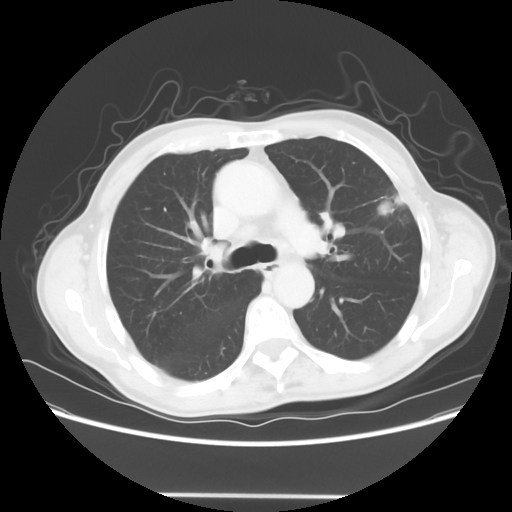
Chest CT, one axial slice; position 41 of 64 along the scan axis; 120 kVp; lung window (W 1500 / L -600 HU); 5 mm slice thickness; 512 × 512 image matrix. Patient: male, 71 years. From the clinical record (not read from this slice): clinical TNM (as recorded): T1c N0 M0; histopathological grade: G2-3.
Annotated regions visible in this slice (bounding box drawn by a radiologist):
- lung tumour (recorded histology: adenocarcinoma): bounding box [x1, y1, x2, y2] px = [372, 186, 407, 225]